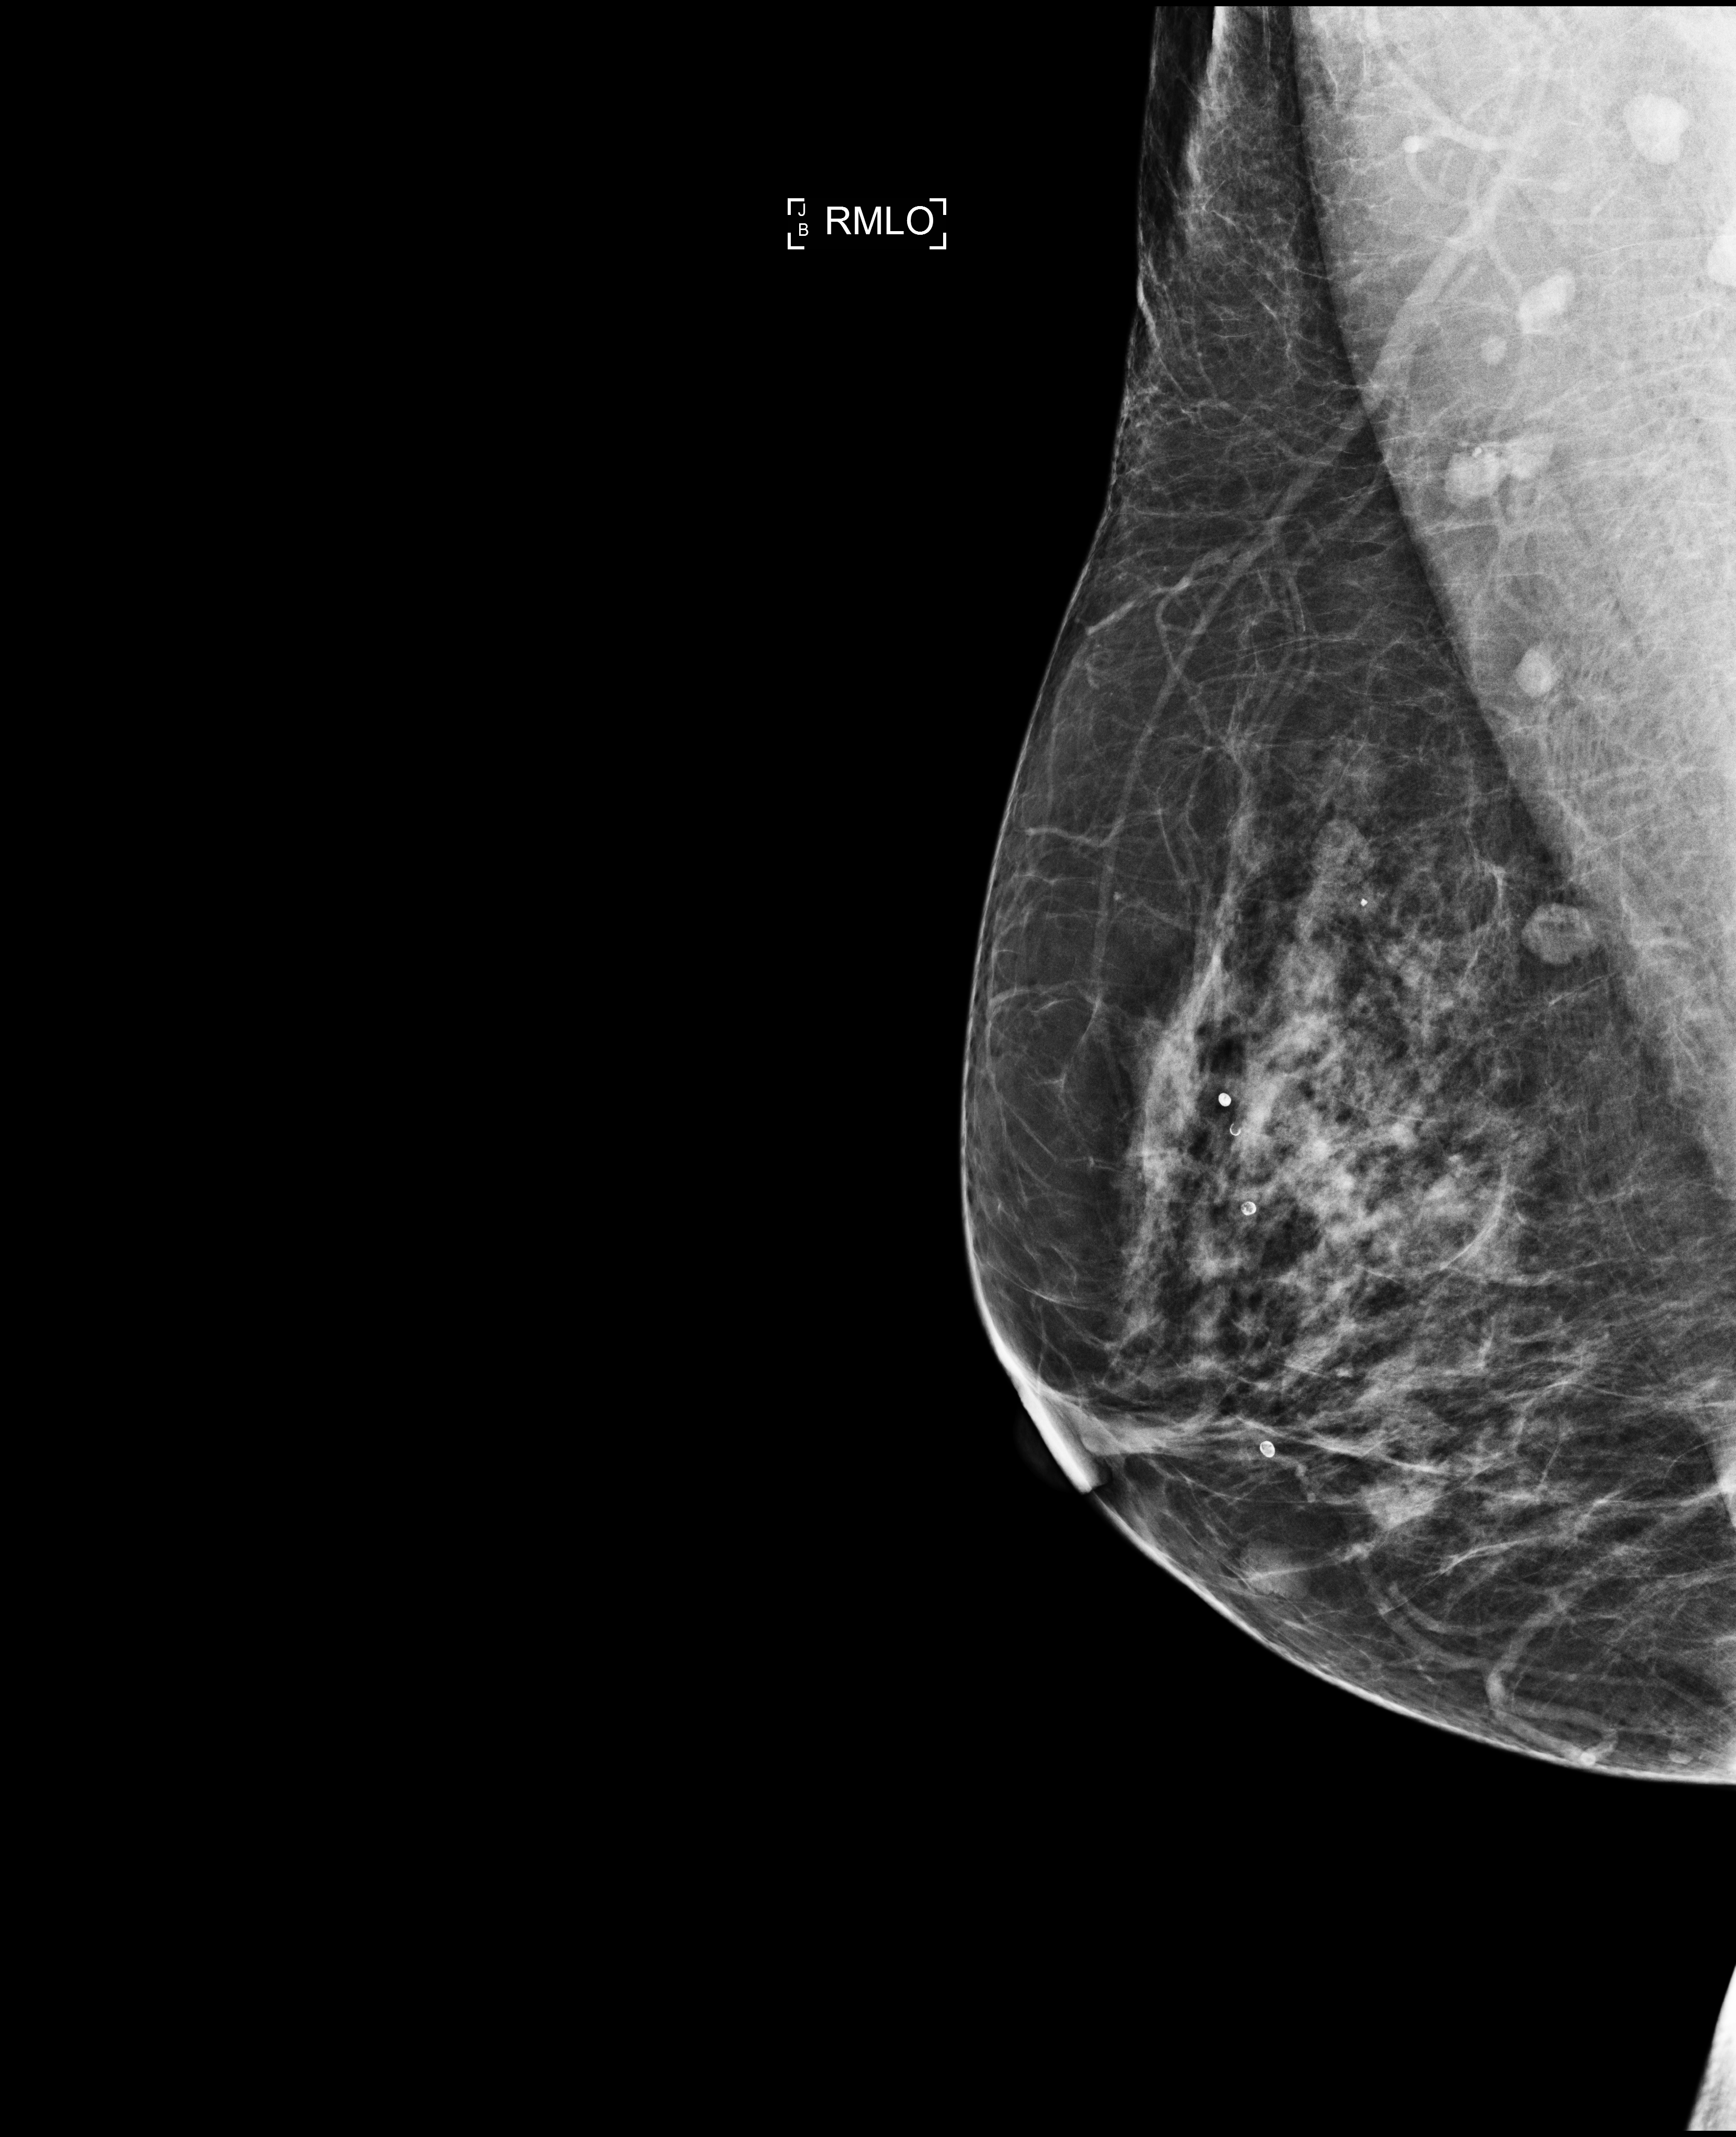
Screening examination, compressed breast thickness 62 mm. Patient: female, 63 years.
Image type: full-field digital mammogram. Breast: right. Projection: mediolateral oblique (MLO) view. BI-RADS breast density category at the screening exam (both breasts, scale 1–4): 2. Final BI-RADS category for the screening round (tomosynthesis exam, both breasts): category 1. Recall: no recall after this screen.